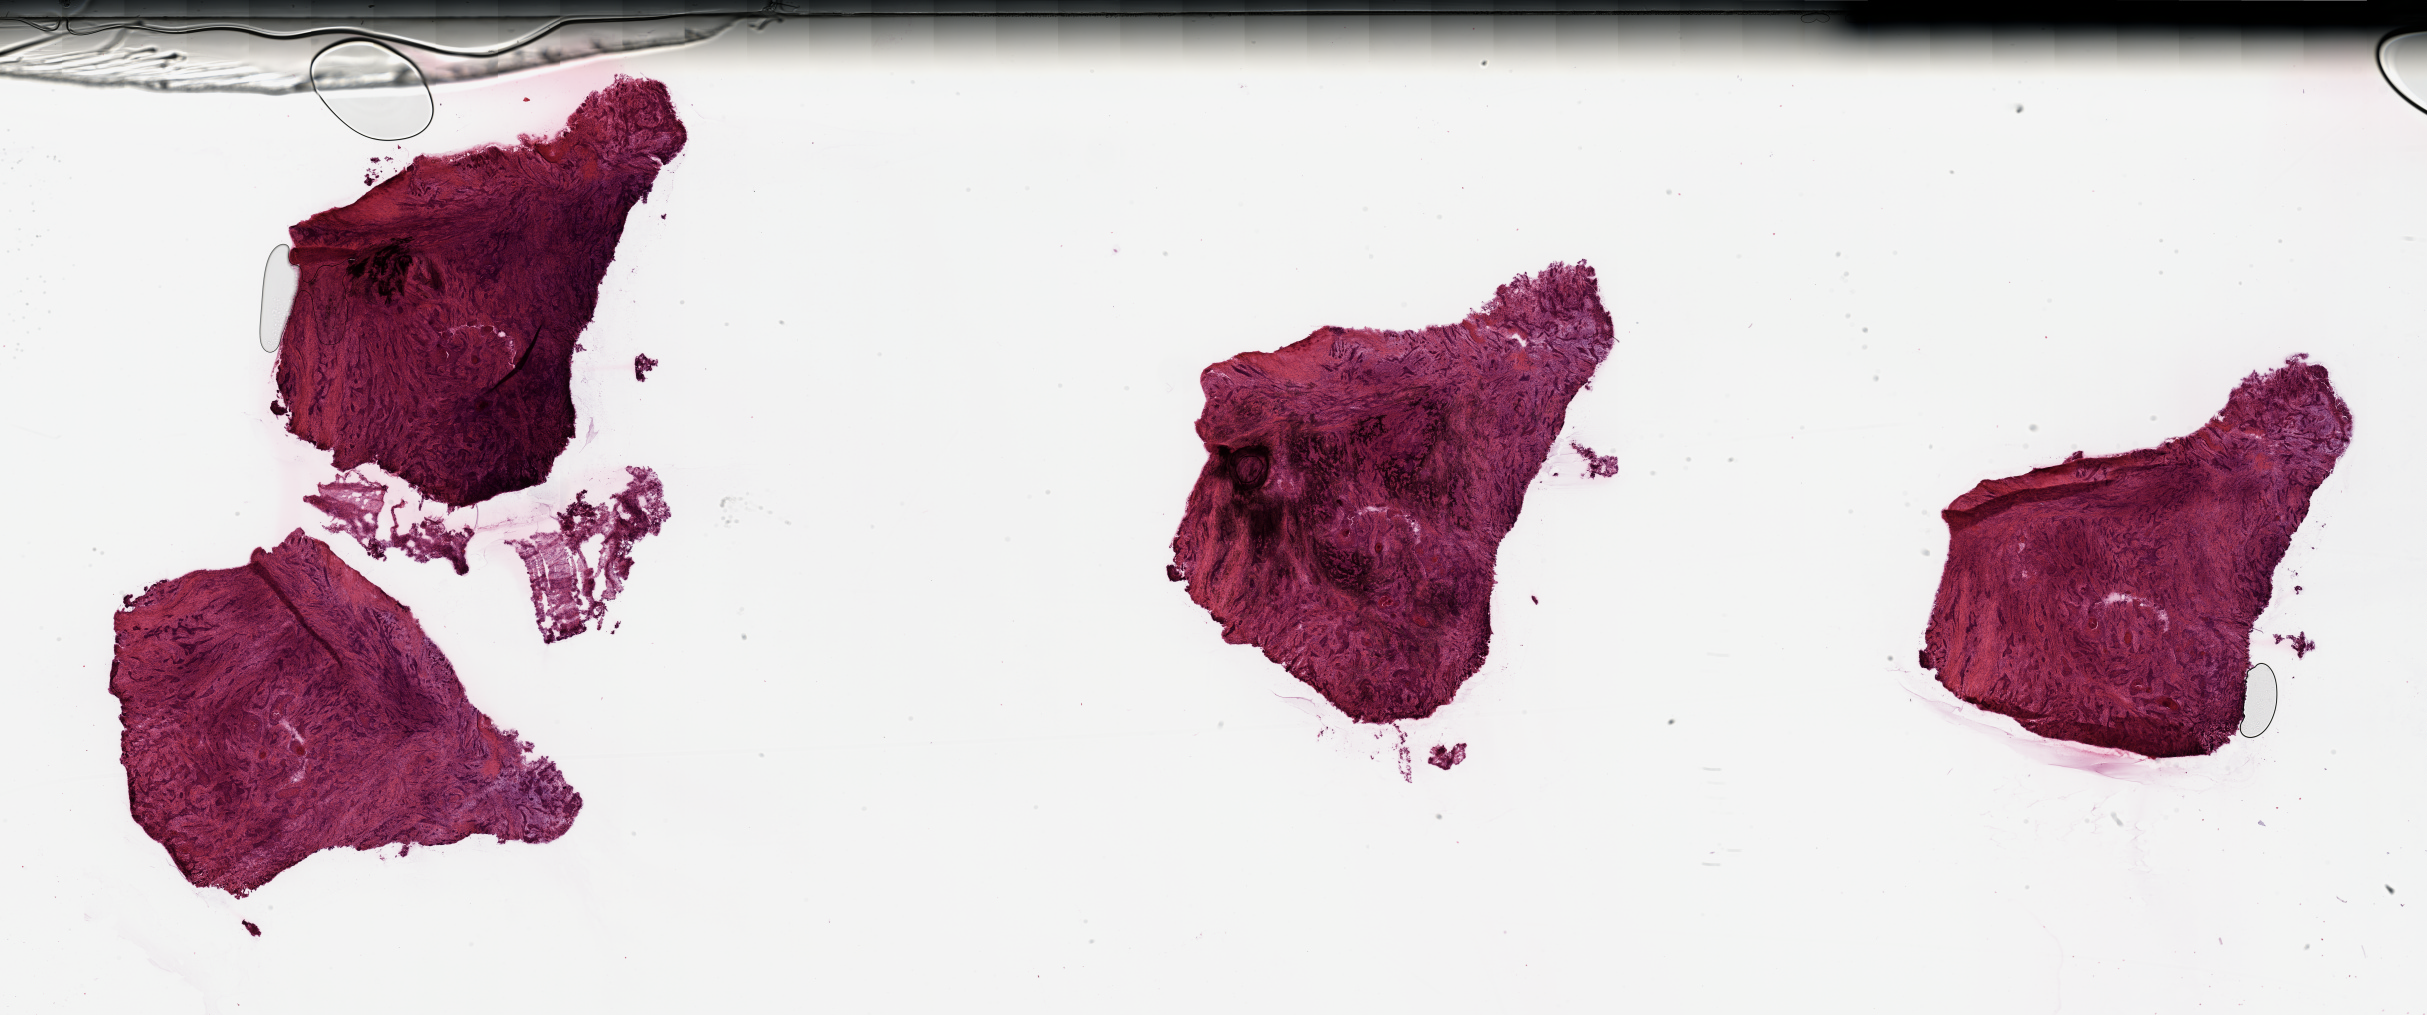
Whole-slide histology image, H&E-stained, low-resolution overview of the scanned area, about 38.4 x 16.1 mm (acquisition: 20x scan). Head and neck, tissue type not recorded. 70-year-old male patient.
Patient diagnosis: Squamous cell carcinoma, NOS (larynx, NOS).